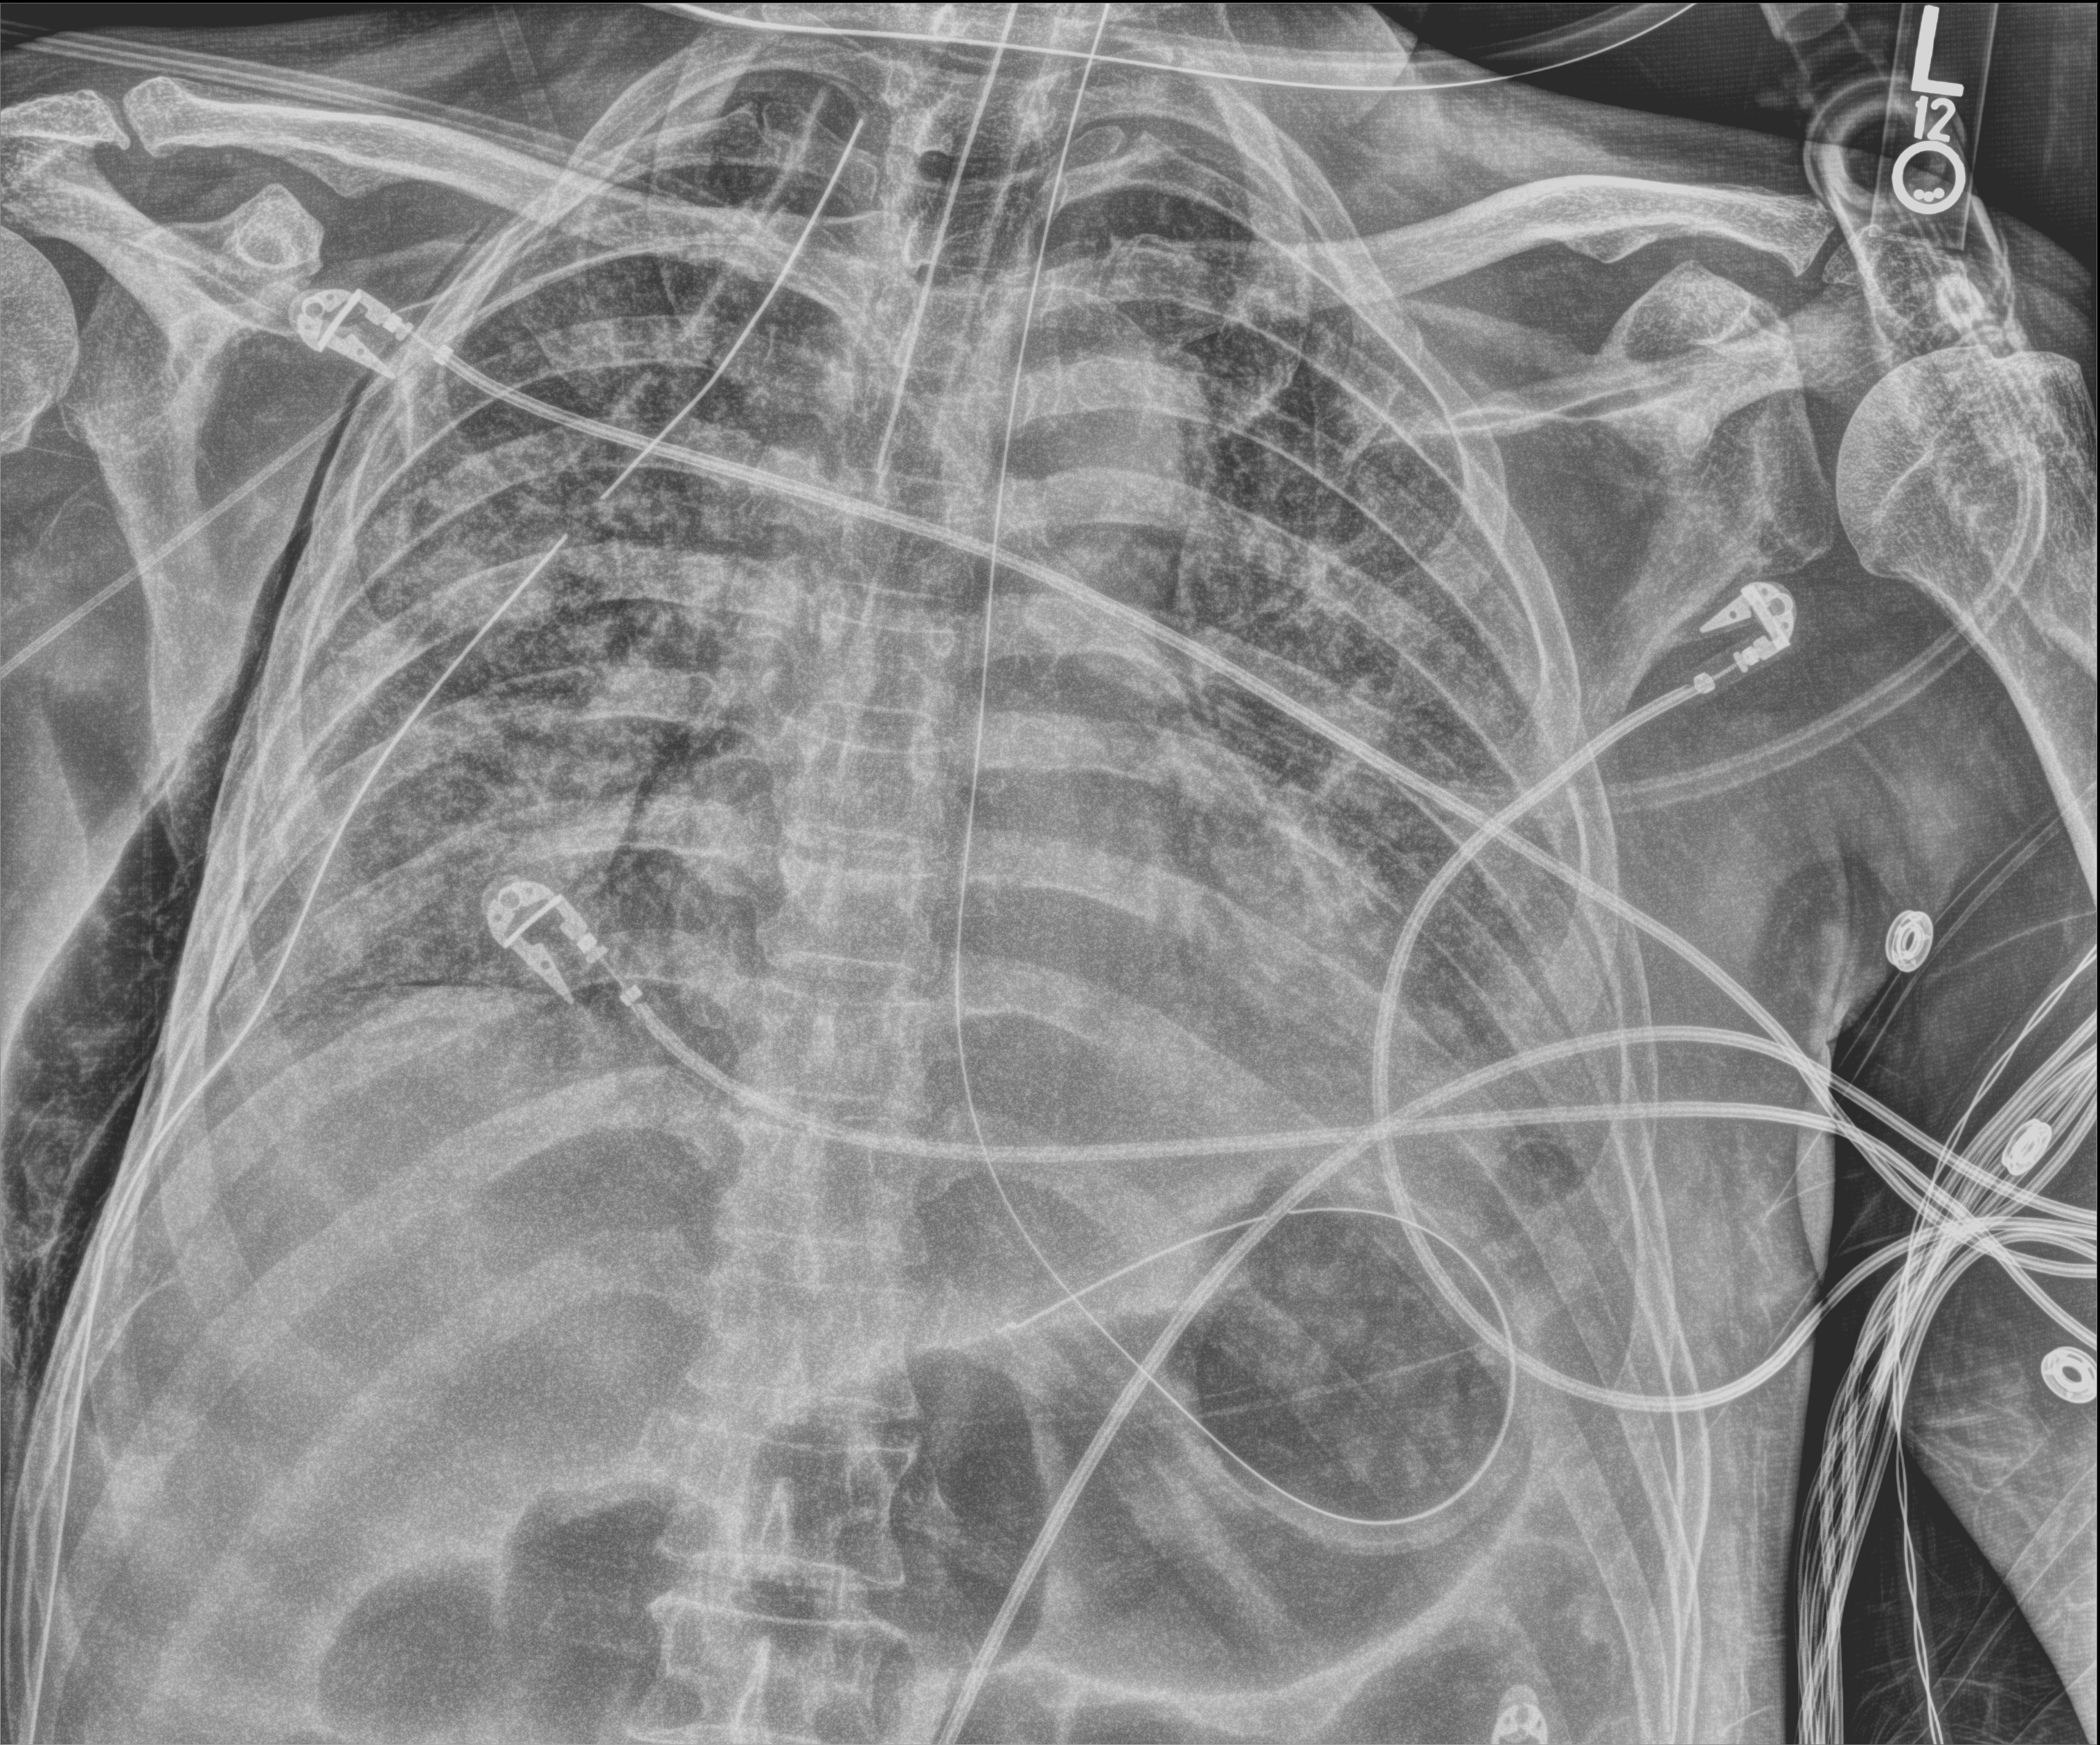
Portable chest radiograph. Patient hospitalised with COVID-19; male, aged 60–74 years.
From the hospital-stay record, not from the radiograph (when in the stay this image was taken is not recorded): length of hospital stay: 37 days.